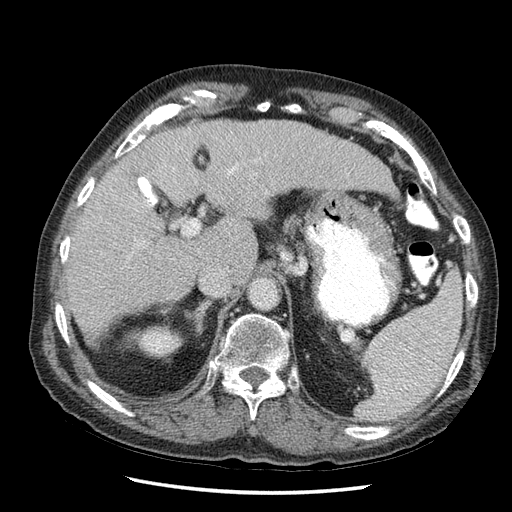
Contrast-enhanced abdominal CT (liver protocol), one axial slice. 120 kVp. Soft-tissue window (W 400 / L 40 HU). 2.5 mm slice thickness. 512 × 512 image matrix. From the clinical record (not read from this slice): diagnosis: hepatocellular carcinoma (patient treated with transarterial chemoembolisation; whether this scan precedes or follows treatment is not stated here); TNM stage (as recorded): Stage-I; Child-Pugh class: A; tumour nodularity: uninodular.
Structures marked on this image (semi-automatic segmentation, software-assisted and operator-edited):
- liver parenchyma outside the tumour (the mass and vessels are separate outlines, so this box may not span the whole liver): bounding box <62,118,398,364> (left, top, right, bottom; pixels)
- liver vessels: <126,144,274,246>